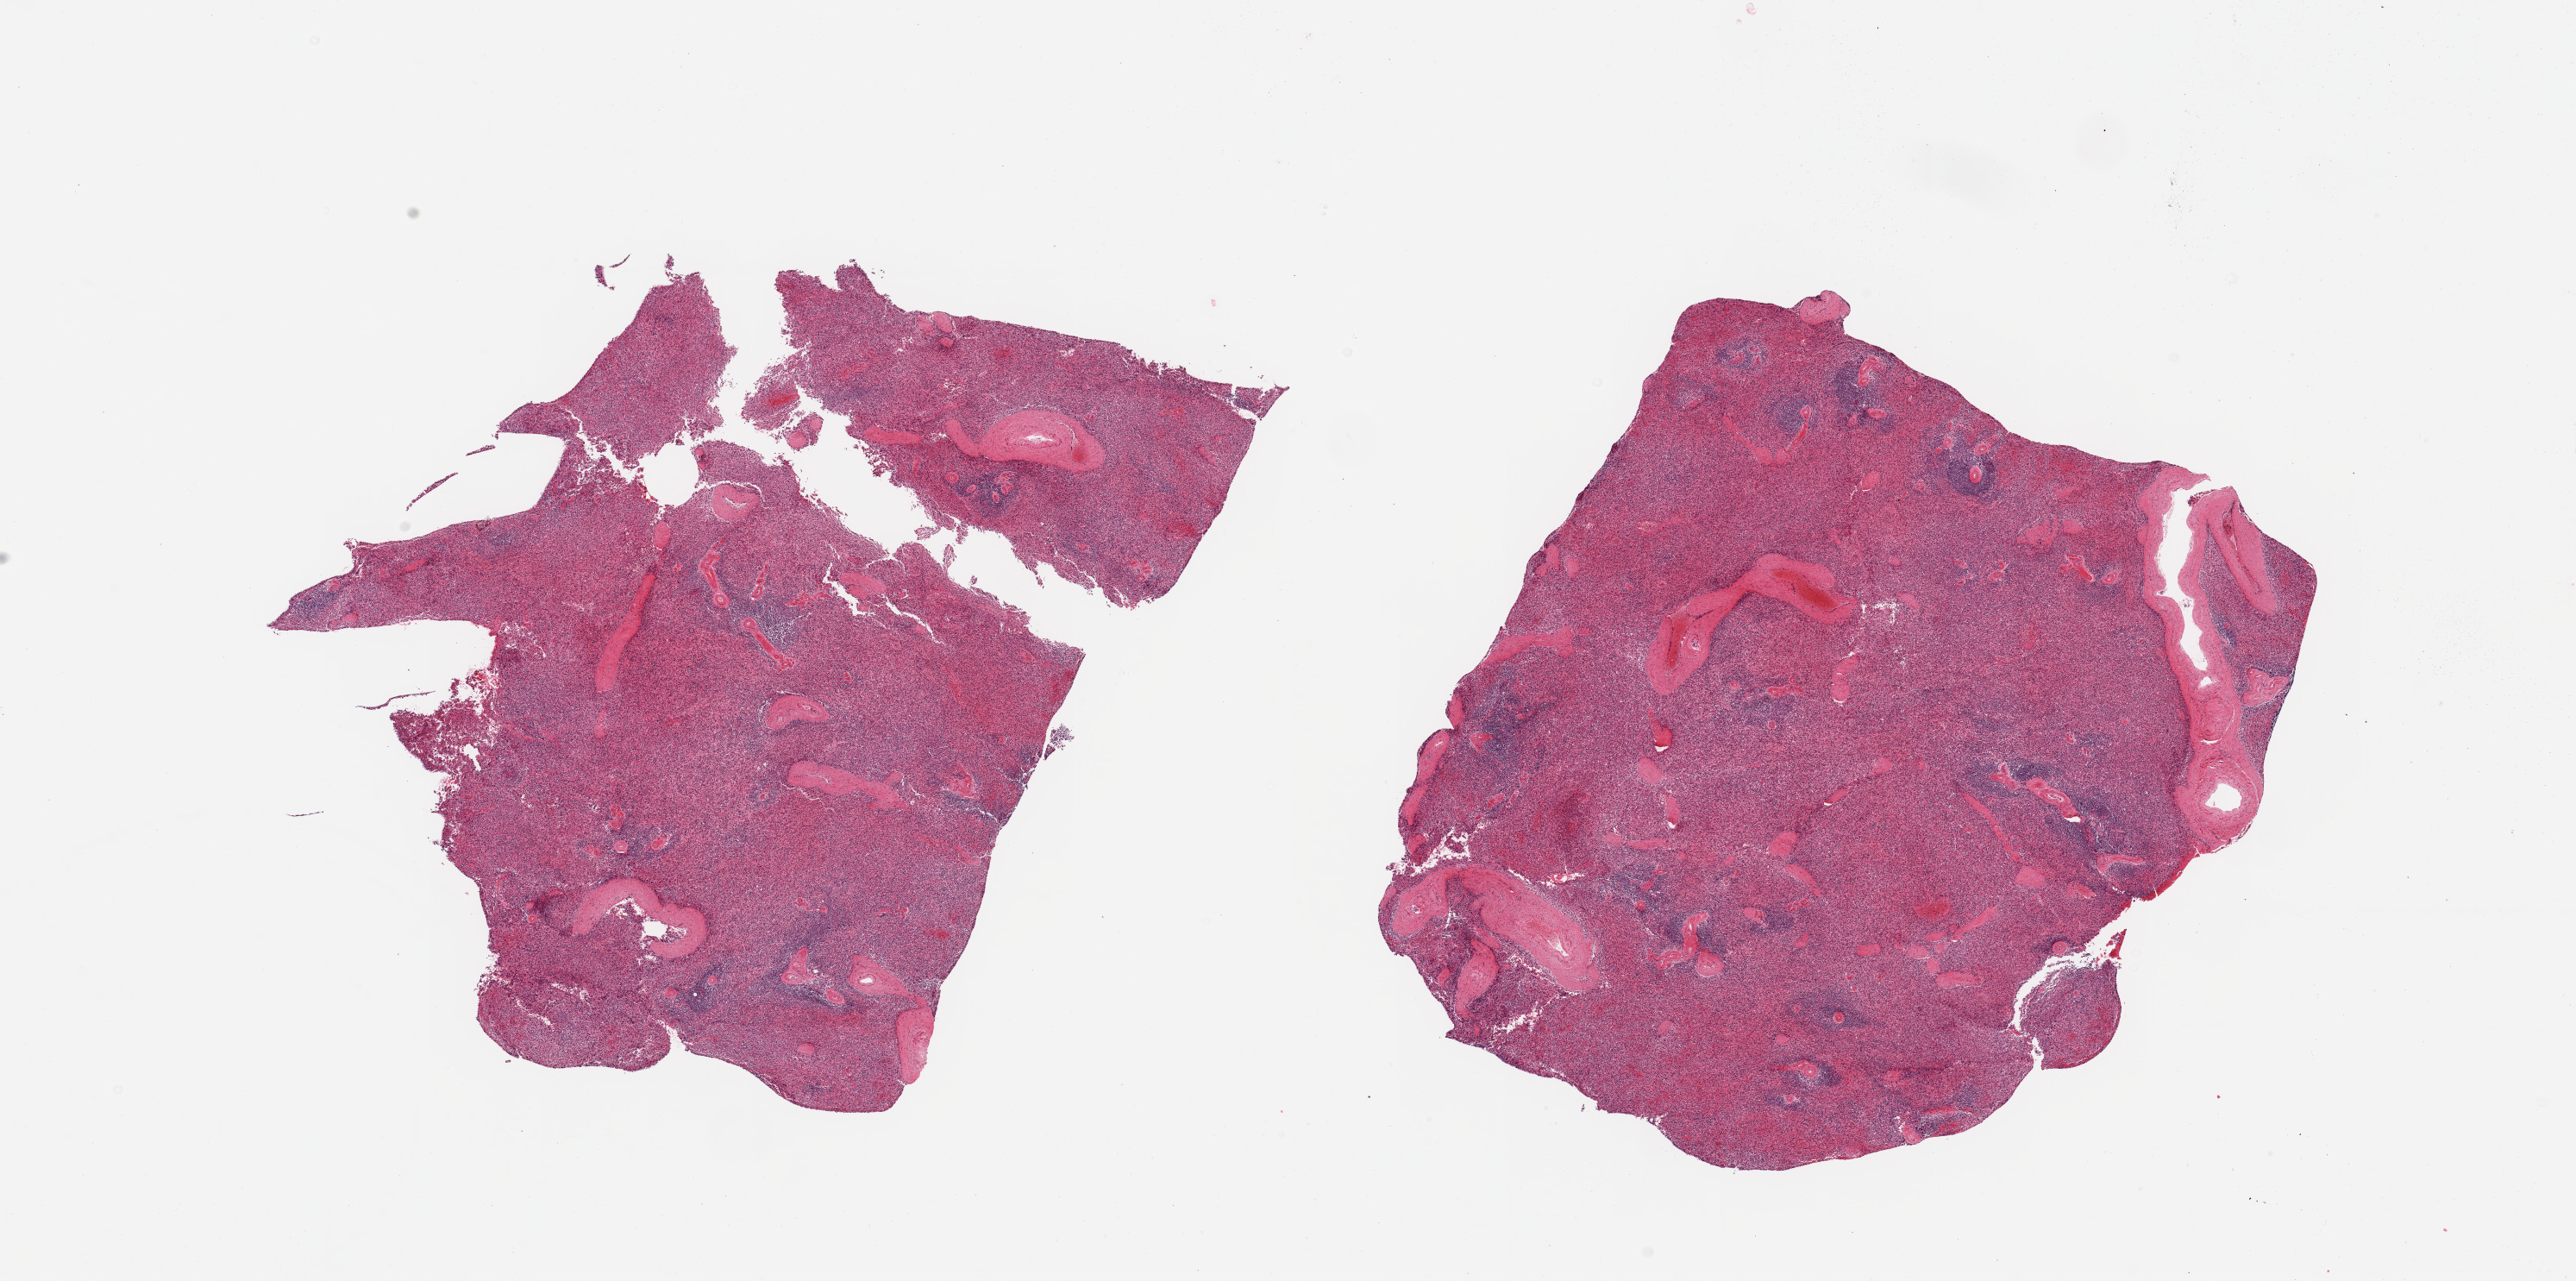
Haematoxylin and eosin whole-slide image — a low-resolution overview of the entire scanned area, about 23.6 x 11.7 mm. PAXgene-fixed paraffin-embedded (PFPE) section. Section of spleen (target tissue). Tissue donor sample.
* review note (as recorded): 2 pieces, moderate congestion